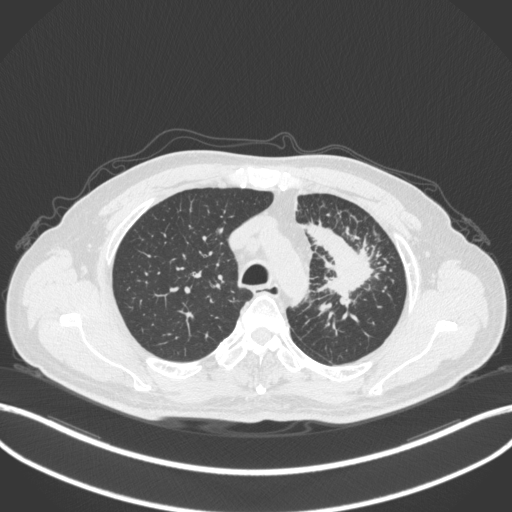
Chest CT, one axial slice; position 272 of 386 along the scan axis; lung window (W 1500 / L -600 HU); 512 × 512 image matrix, field of view 400 × 400 mm. Male patient, age 69 years. From the clinical record (not read from this slice): clinical TNM (as recorded): T2a N2 M0; histopathological grade: G2-3.
Structures marked on this image (rectangle marked by the reading radiologist):
- lung tumour (recorded histology: adenocarcinoma): bounding box <305,218,375,300> (left, top, right, bottom; pixels)